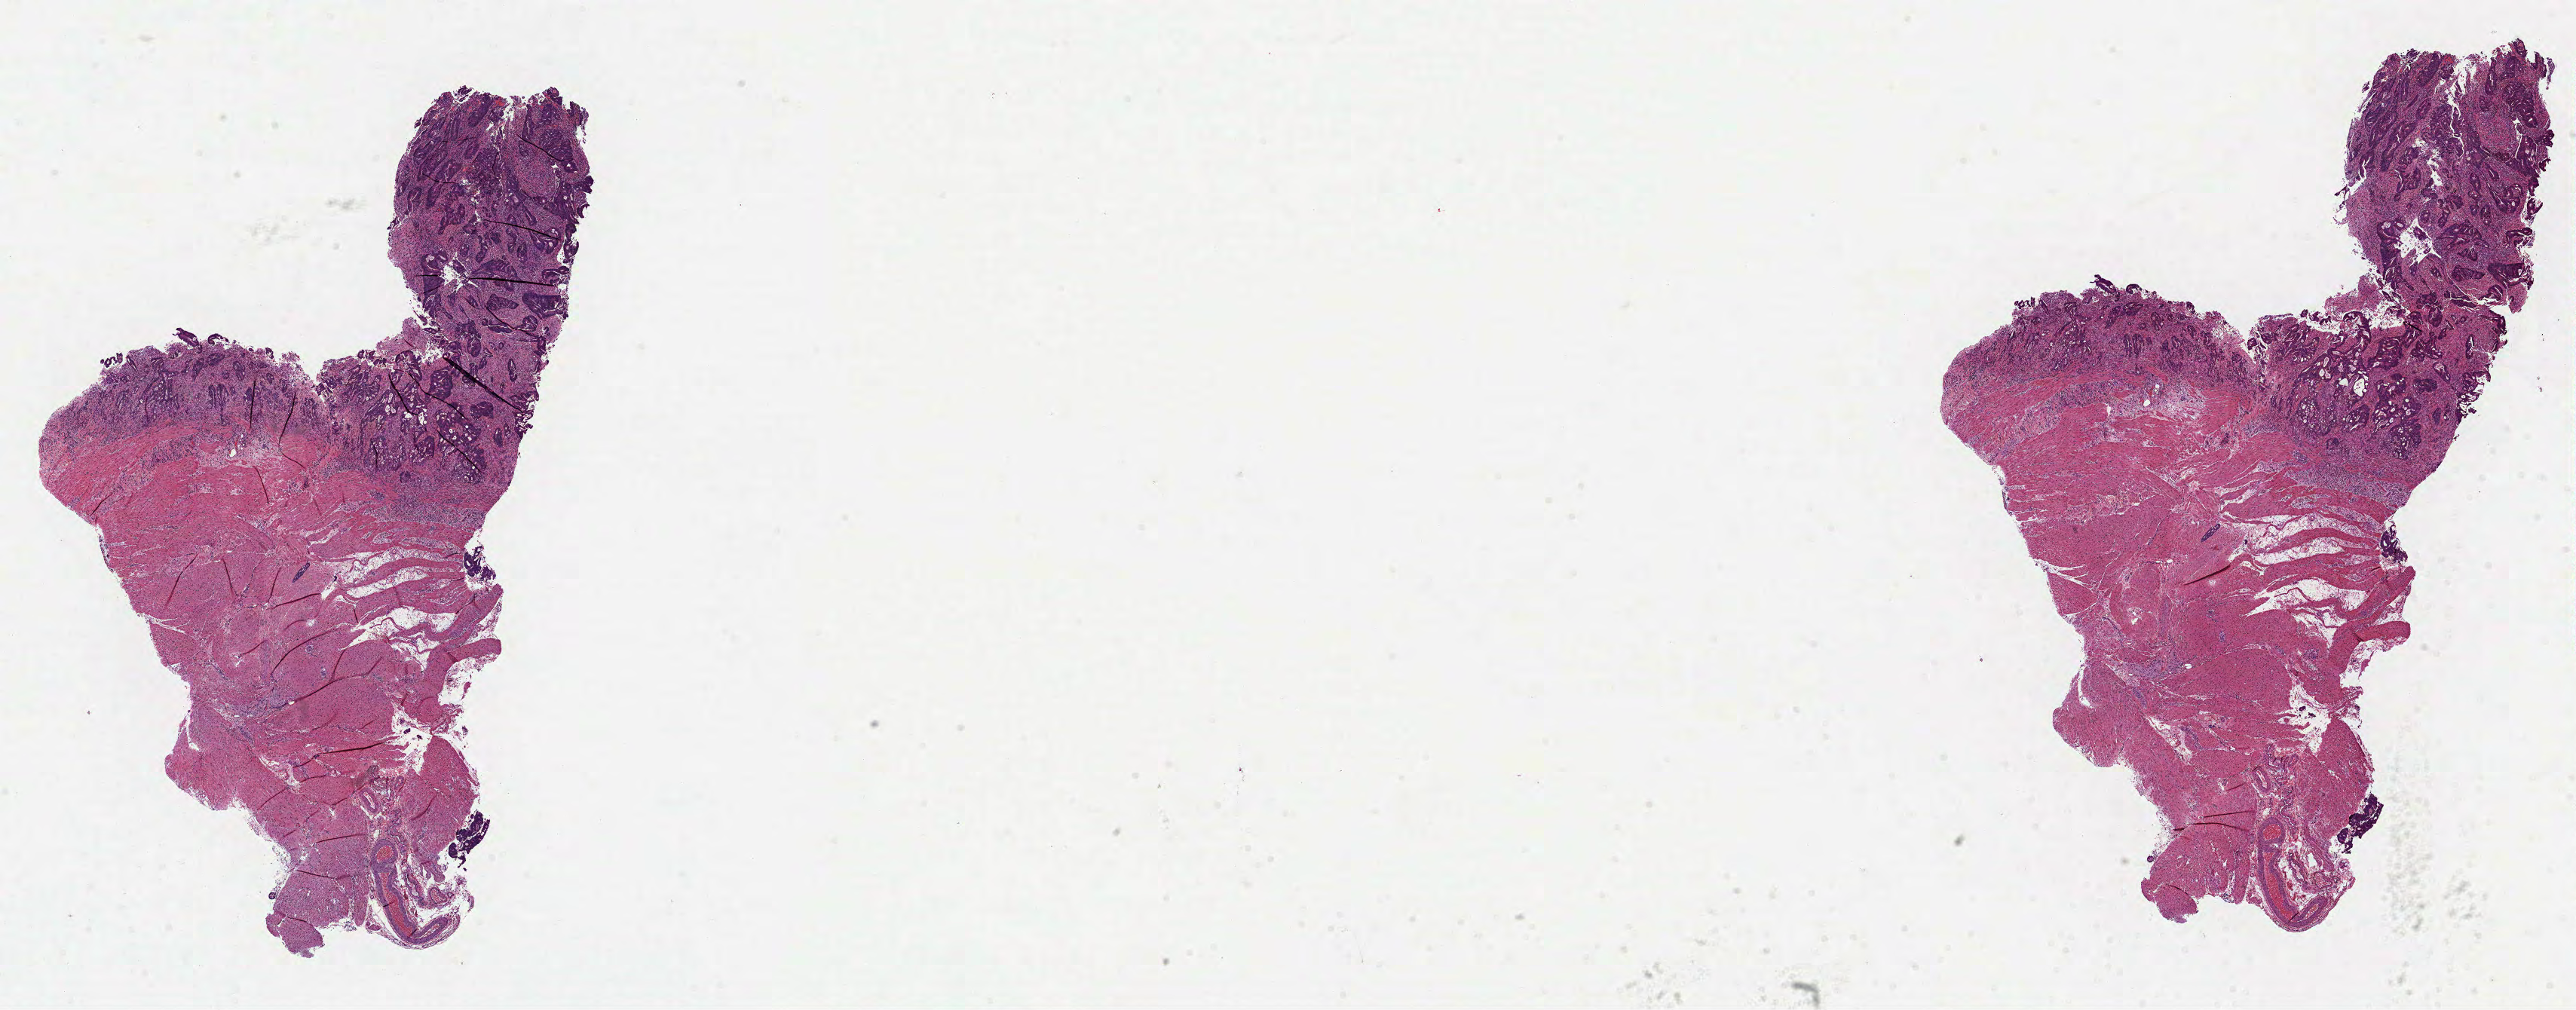
H&E whole-slide image, low-resolution overview of the scanned area, about 27.6 x 10.8 mm, formalin-fixed paraffin-embedded (FFPE) diagnostic section, sample: primary tumour, colon. Female, age 75 years at initial diagnosis.
AJCC pathologic stage: I. Histologic diagnosis: Adenocarcinoma, NOS. Lymph nodes positive (case pathology): 0 of 33 examined.